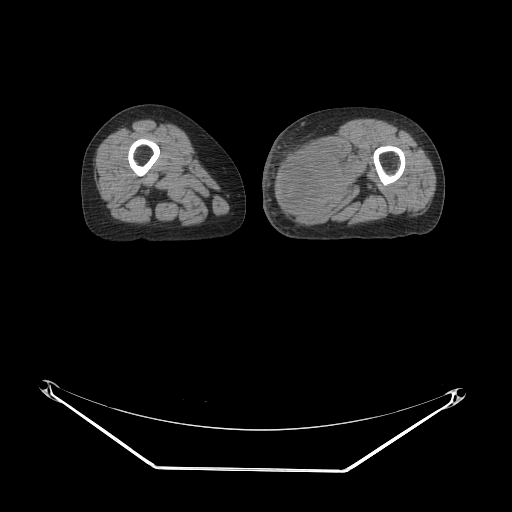
CT of an extremity soft-tissue mass (from a PET/CT study), one axial slice. Slice 23 of 91 in the series (ordered by position). Reconstruction kernel STANDARD. Soft-tissue window (W 400 / L 40 HU). 3.75 mm slice thickness. 512 × 512 image matrix, field of view 500 × 500 mm. Female patient. Case-level facts recorded for this patient, not image findings: histological type: pleomorphic leiomyosarcoma; grade: high; site of the primary tumour: left thigh.
Annotated regions visible in this slice (expert contour drawn on MRI and transferred to this co-registered scan by the dataset authors):
- gross tumour volume including surrounding oedema: bounding box [x1, y1, x2, y2] px = [276, 135, 359, 216]
- gross tumour volume (mass): [276, 148, 353, 215]